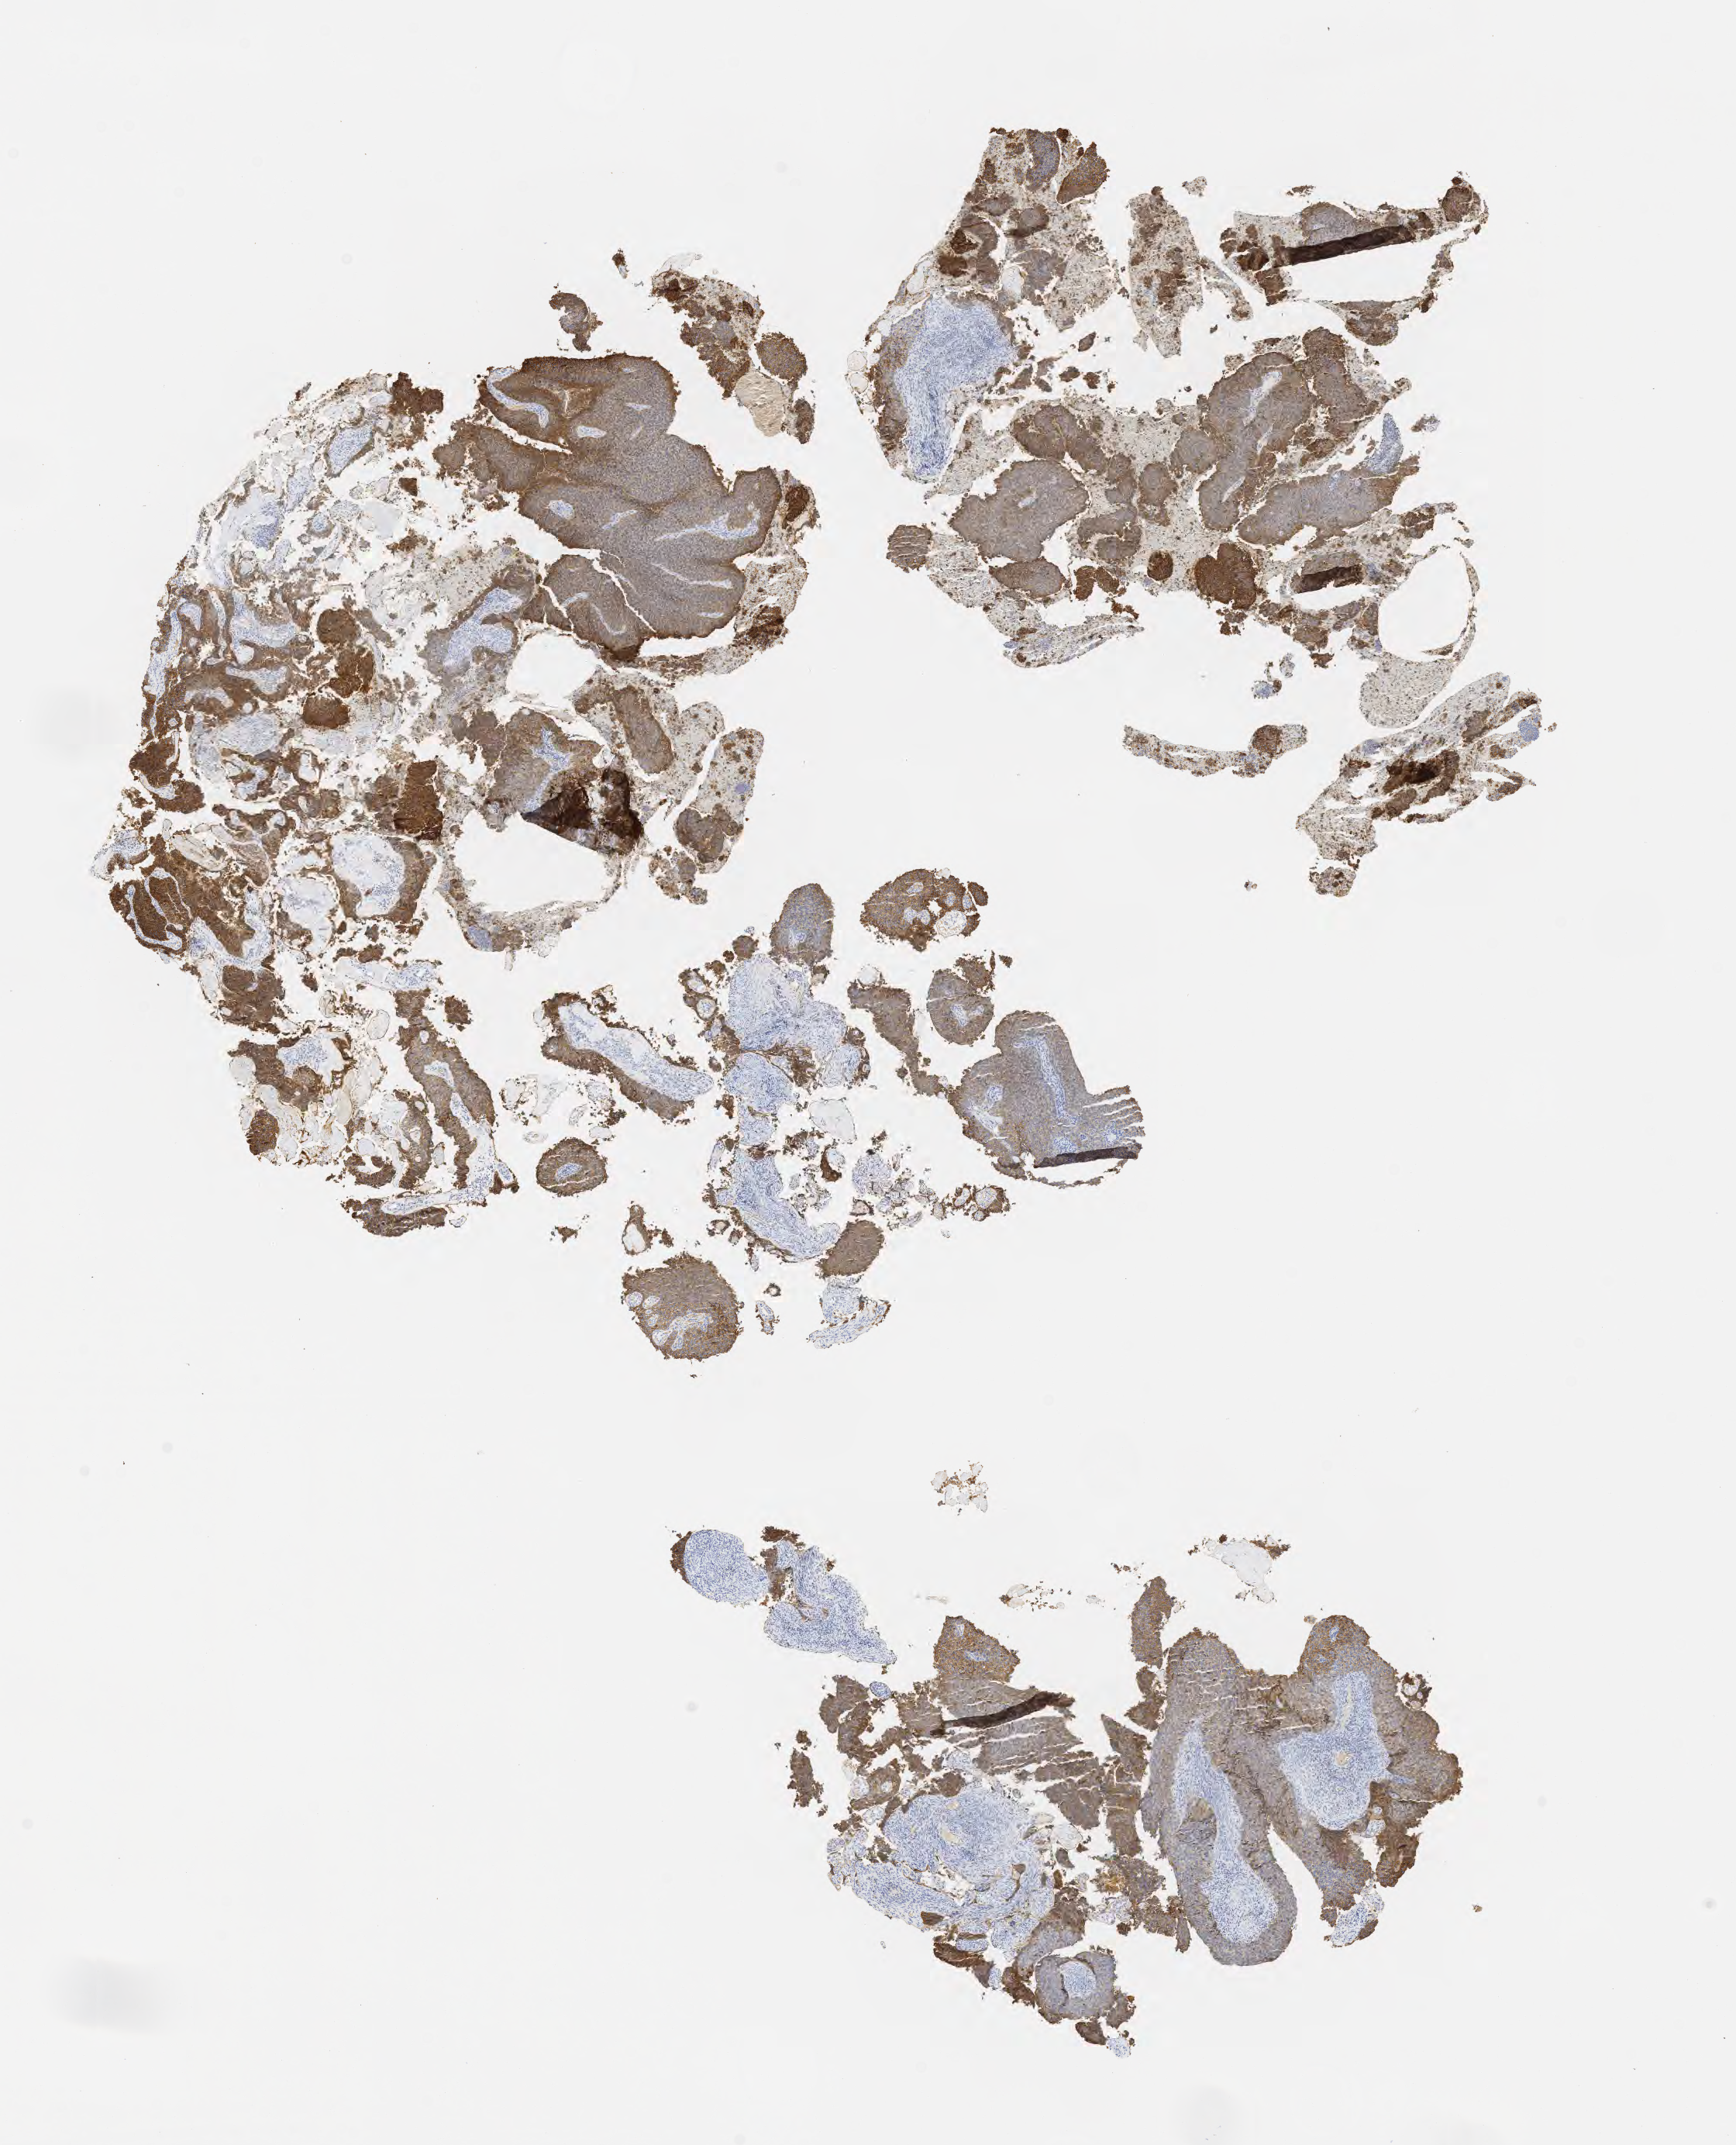
Immunohistochemistry (IHC) whole-slide image stained for Ber-EP4, whole scanned area (about 9.1 x 11.2 mm) shown as a low-resolution overview. Tumor tissue. Anatomic site: cervix. Patient female; aged 44.
Diagnosis: Squamous cell carcinoma, large cell, nonkeratinizing, NOS.